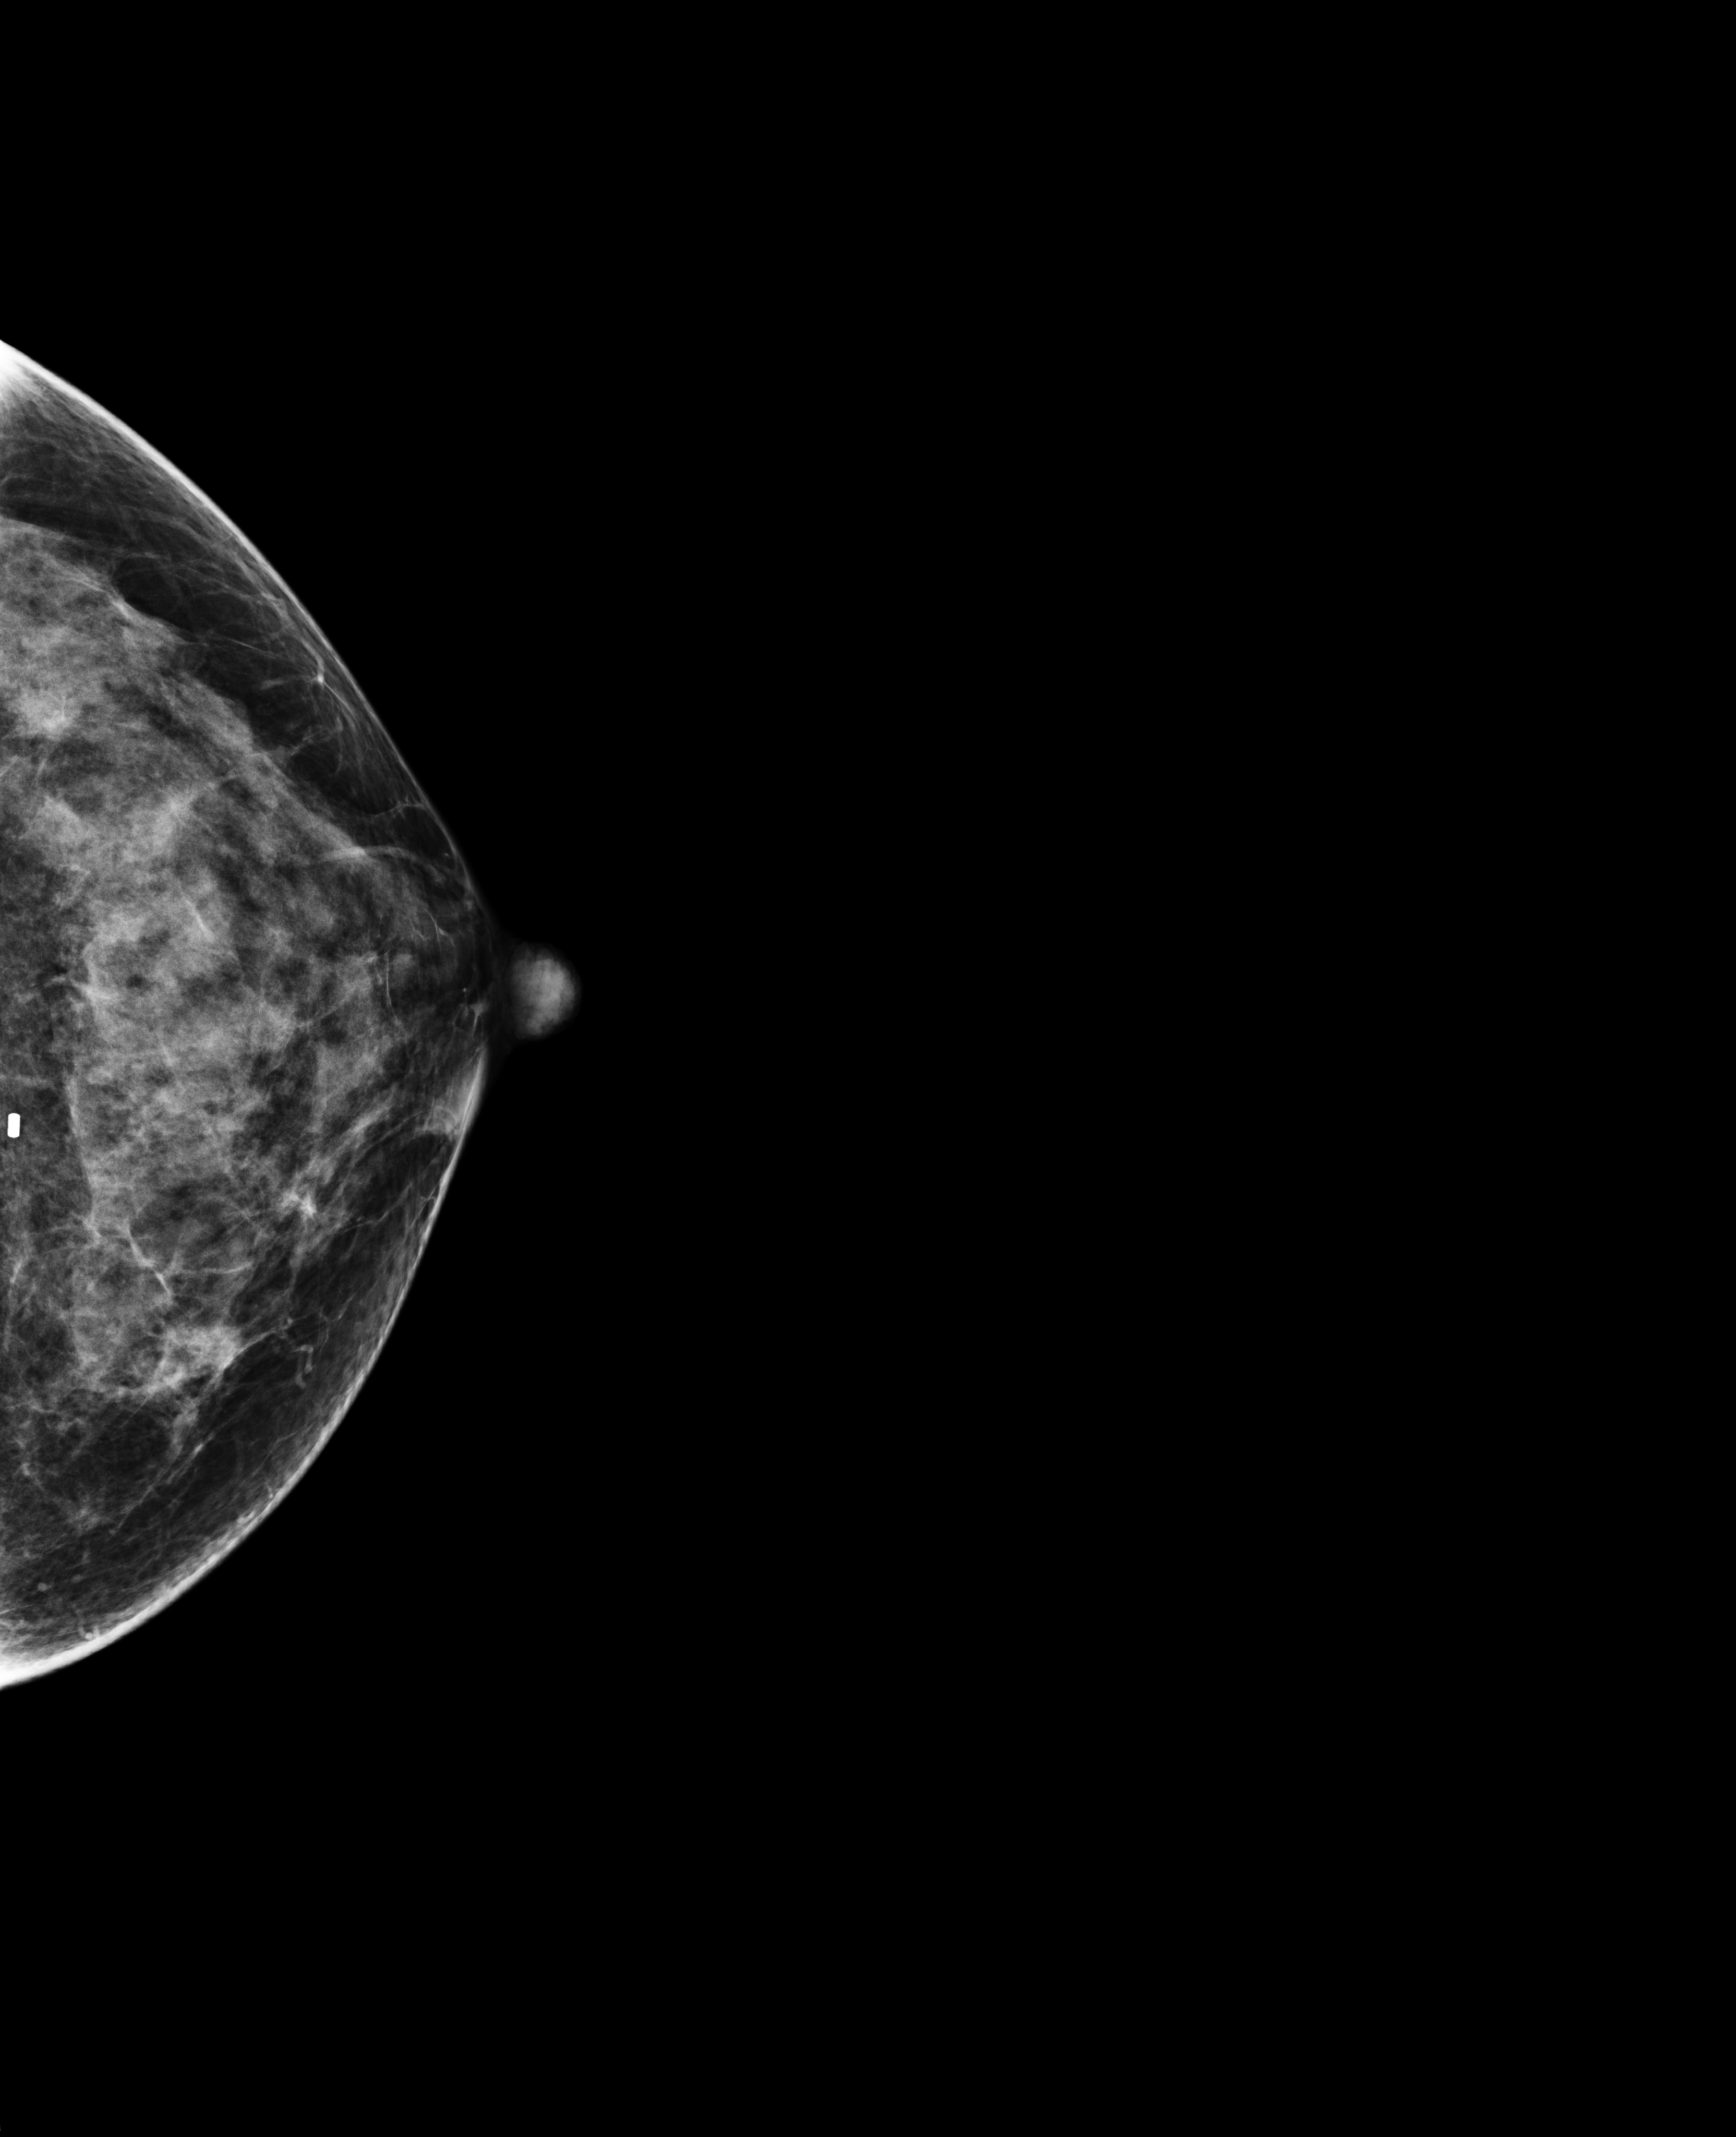
Annual screening mammography examination. Female patient, age 42 years.
Image type: full-field digital mammogram. Breast: left. Projection: CC view.